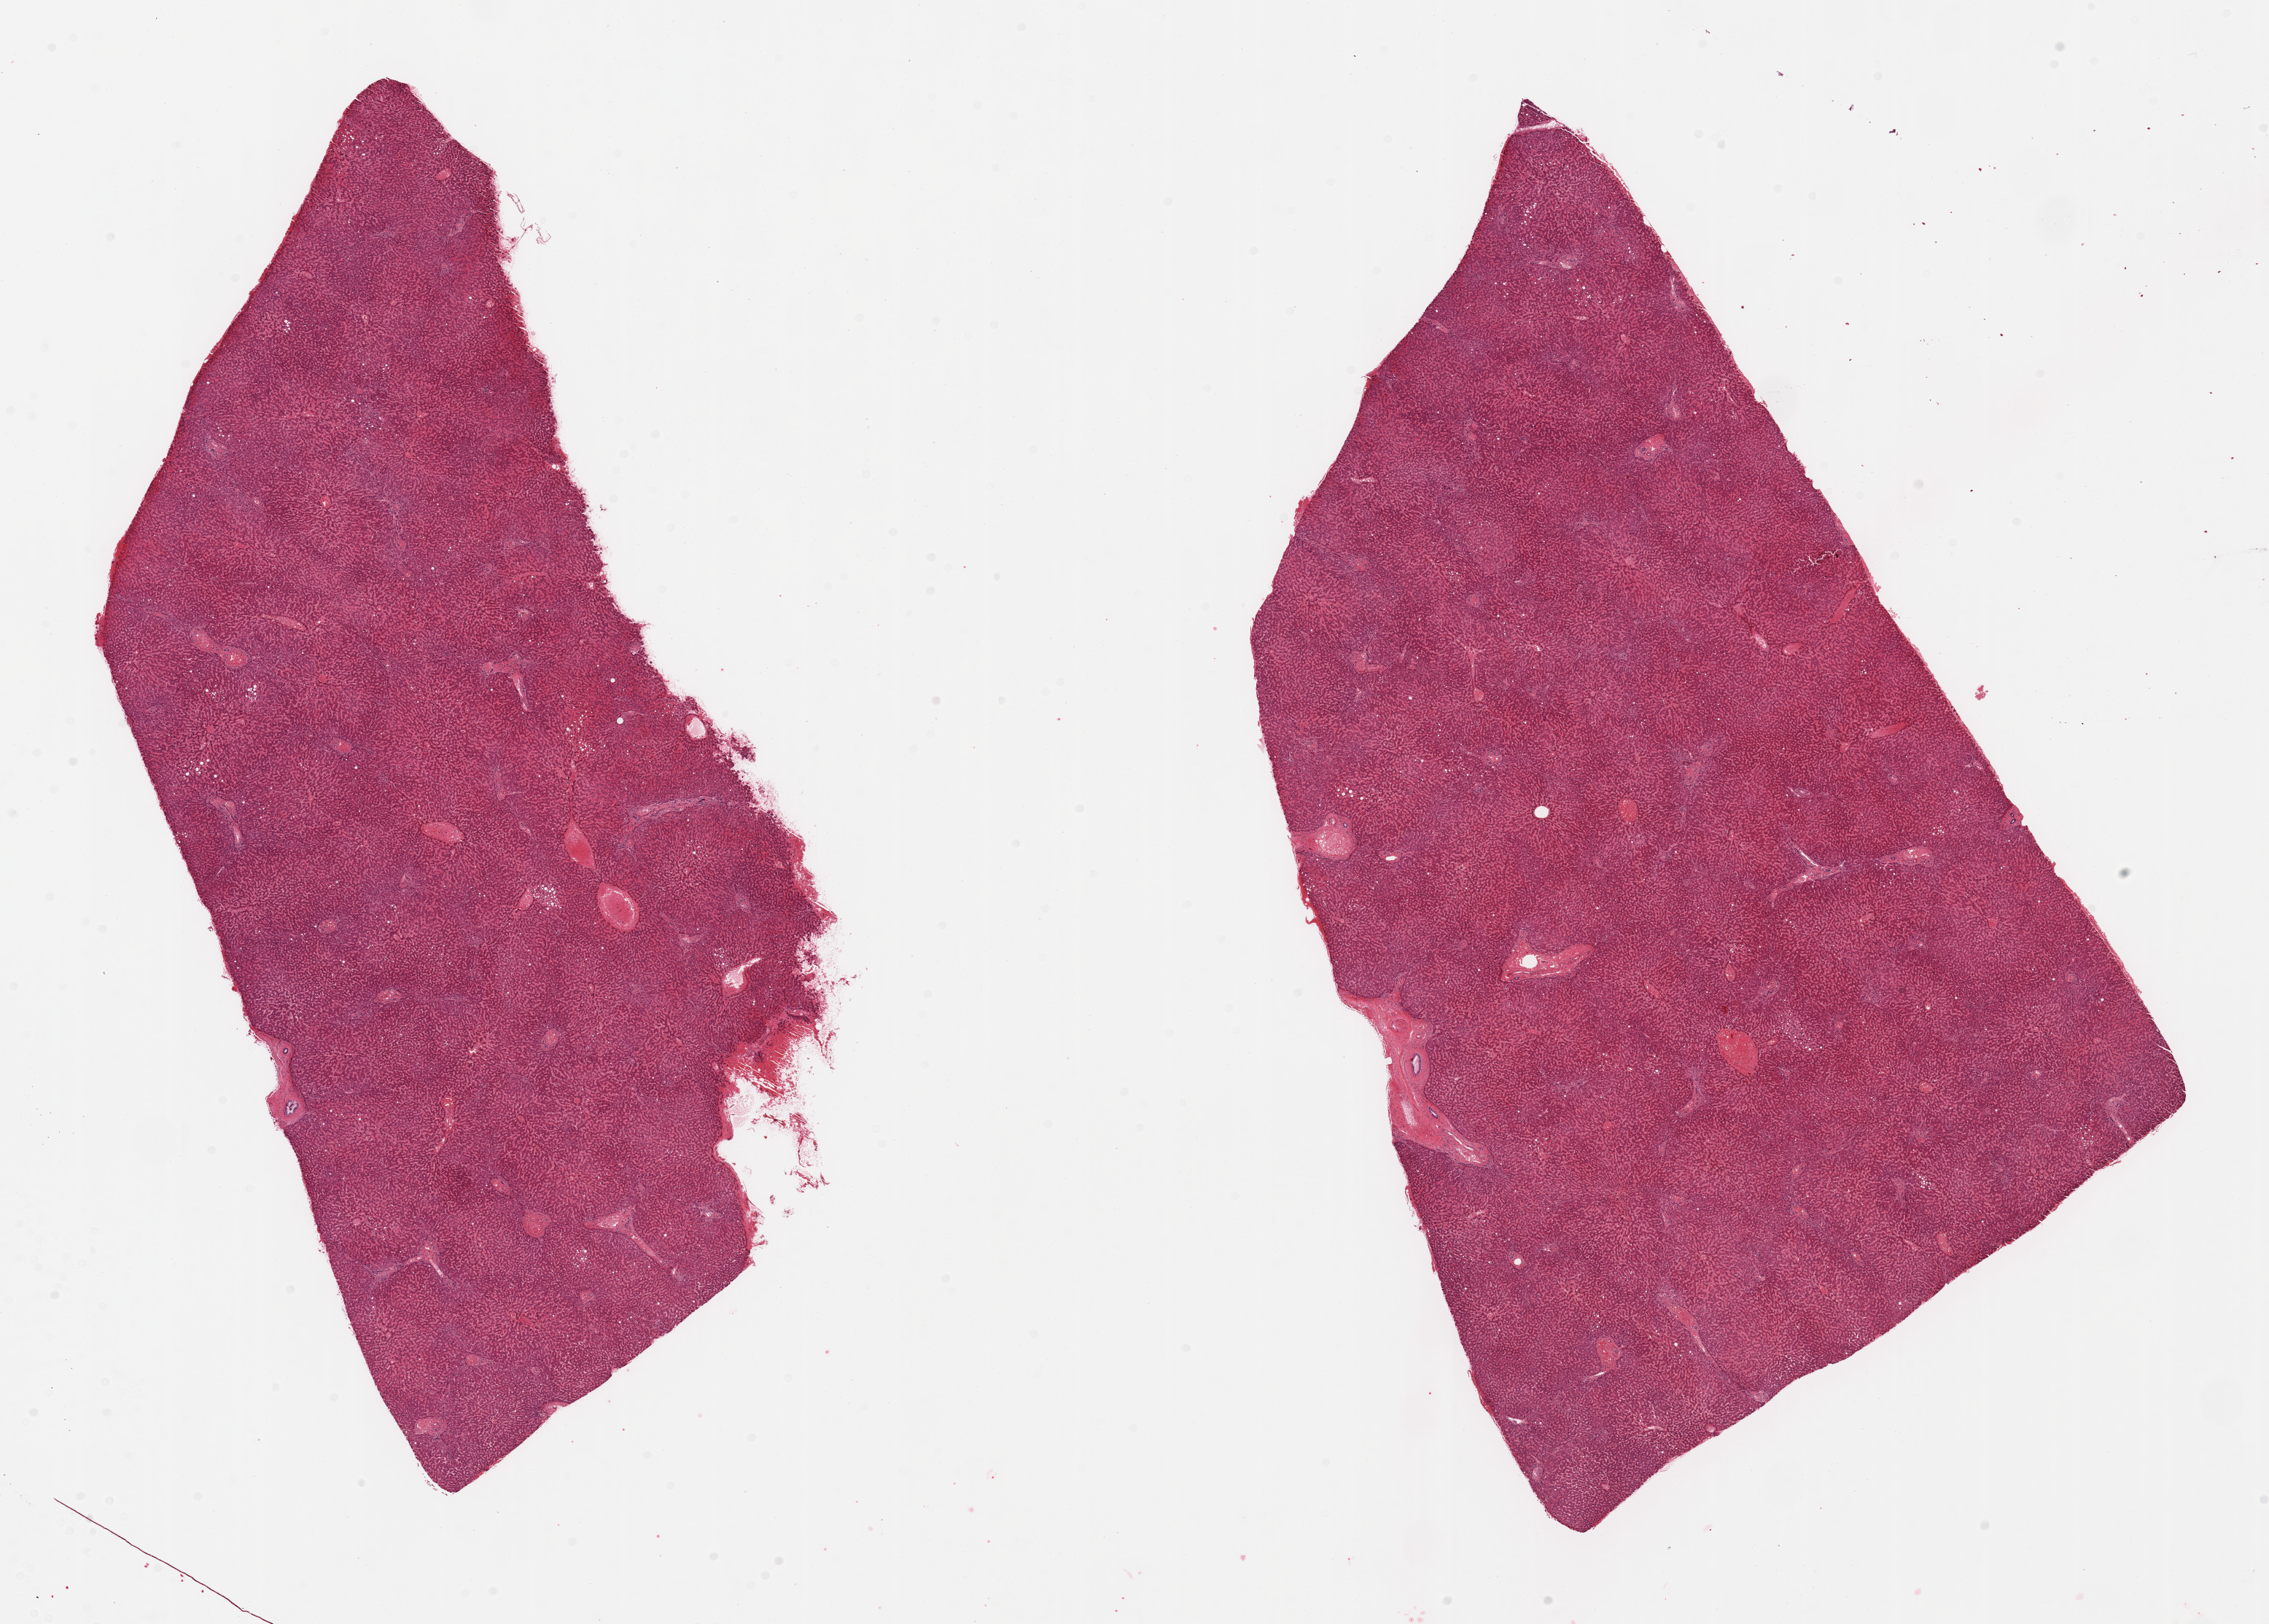
Haematoxylin and eosin whole-slide image — low-resolution overview of the scanned area, about 24.6 x 17.6 mm; PAXgene-fixed, paraffin-embedded tissue; sampled site (target tissue): liver; tissue donor sample. Male donor.
Reviewer comment on this tissue sample: 2 pieces; moderate centrilobular congestion.